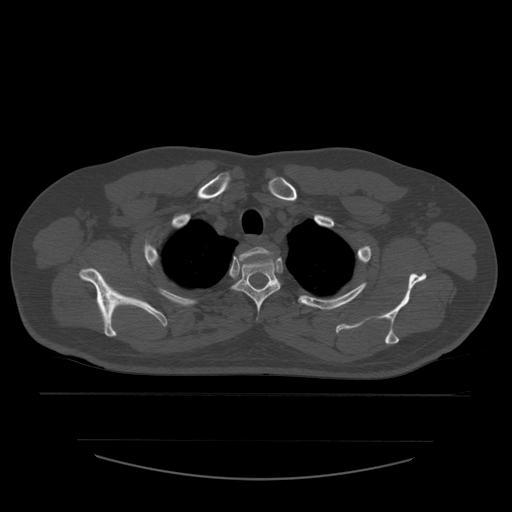
CT including the spine, one axial slice; position 452 of 532 along the scan axis; bone window (W 1800 / L 400 HU); 1.25 mm slice thickness; 512 × 512 image matrix, field of view 441 × 441 mm. Patient age 44 years. From the clinical record (not read from this slice): primary cancer: soft tissue sarcoma.
Structures marked on this image (semi-automatically segmented with operator editing):
- T1 vertebra: bounding box (x1, y1, x2, y2) in pixels: (239, 247, 274, 270)
- T2 vertebra: (232, 253, 281, 320)